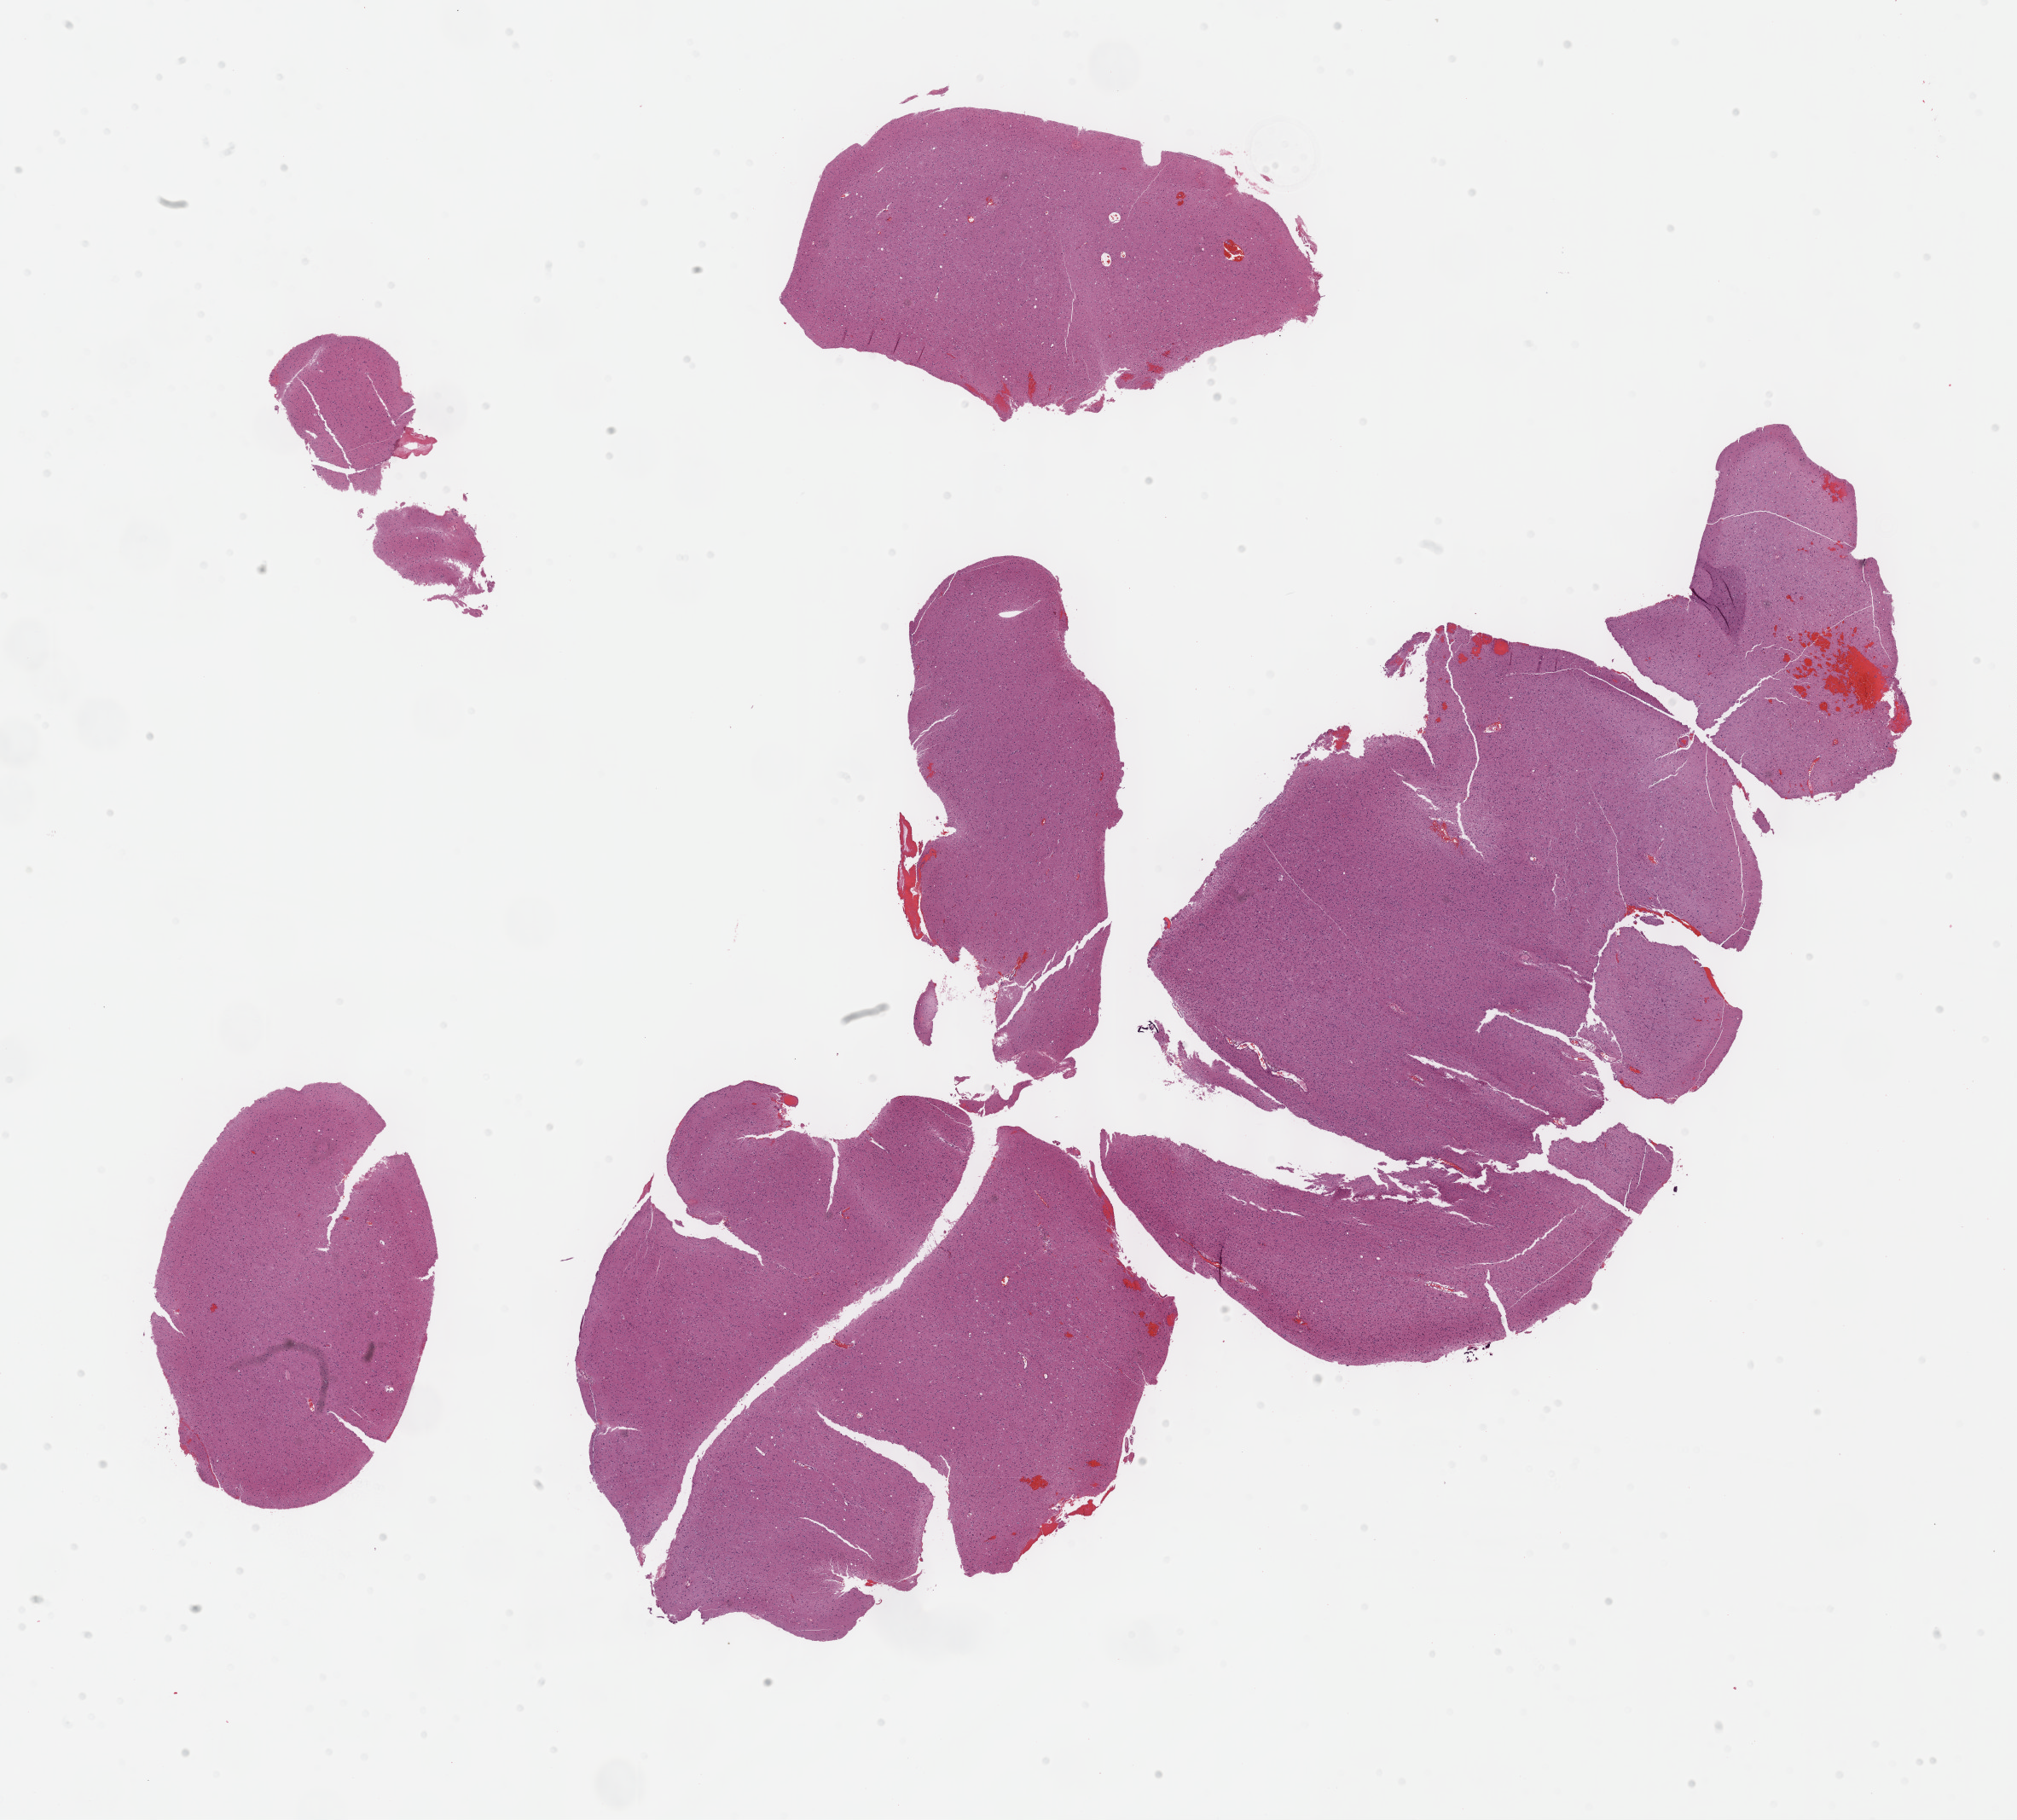
Digitized H&E-stained tissue section (whole slide) — whole scanned area (about 19.1 x 17.3 mm, slide scanned at 40x) shown as a low-resolution overview, FFPE section, primary tumour sample from the brain. Patient: female, age at initial diagnosis 30 years. Histologic grade: G2 (moderately differentiated).
* laterality: right
* pathologic diagnosis: Mixed glioma (cerebrum)